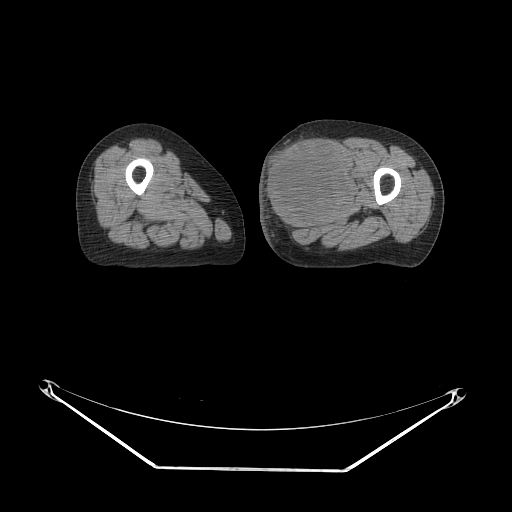
CT of an extremity soft-tissue mass (from a PET/CT study), one axial slice; slice 33 of 91 in the series (ordered by position); reconstruction kernel STANDARD; 140 kVp; soft-tissue window (W 400 / L 40 HU); 3.75 mm slice thickness; 512 × 512 image matrix, field of view 500 × 500 mm. Female patient. From the clinical record (not read from this slice): histological type: pleomorphic leiomyosarcoma; grade: high; site of the primary tumour: left thigh.
Structures marked on this image (expert contour drawn on MRI and transferred to this co-registered scan by the dataset authors):
- gross tumour volume including surrounding oedema: bounding box <263,133,357,232> (left, top, right, bottom; pixels)
- gross tumour volume (mass): <263,135,353,229>